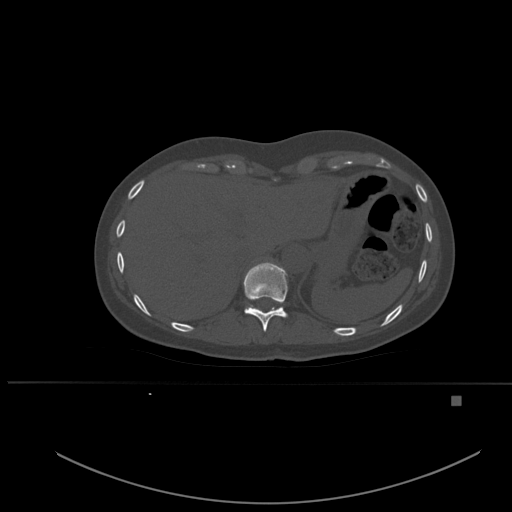
CT including the spine, one axial slice; position 287 of 651 along the scan axis; bone window (W 1800 / L 400 HU); 1.5 mm slice thickness; 512 × 512 image matrix. Patient: female, 49 years. Case-level facts recorded for this patient, not image findings: primary cancer: breast.
Annotated regions visible in this slice (semi-automatic segmentation, software-assisted and operator-edited):
- T10 vertebra: bounding box [x1, y1, x2, y2] px = [244, 262, 288, 332]